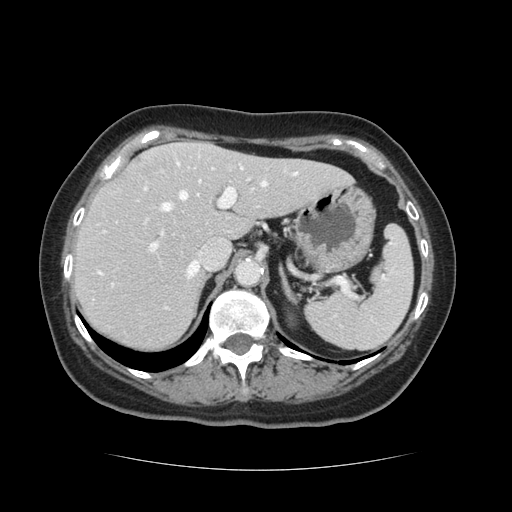
Contrast-enhanced abdominal CT, one axial slice. Slice 87 of 128 in the series (ordered by position). Intravenous contrast given. Soft-tissue window (W 400 / L 40 HU). 512 × 512 image matrix. Female patient, age 67 years. From the clinical record (not read from this slice): diagnosis: colorectal cancer liver metastases, imaged before liver resection; multiple liver metastases: yes; largest metastasis: 3 cm; disease in both lobes: yes.
Outlined on this slice (outlined manually by an expert reader):
- hepatic veins: bounding box <162,167,298,277> (left, top, right, bottom; pixels)
- liver: <74,144,350,351>
- planned liver remnant (the part of the liver to remain after resection): <74,158,349,351>
- portal vein (with intrahepatic branches): <152,167,251,249>